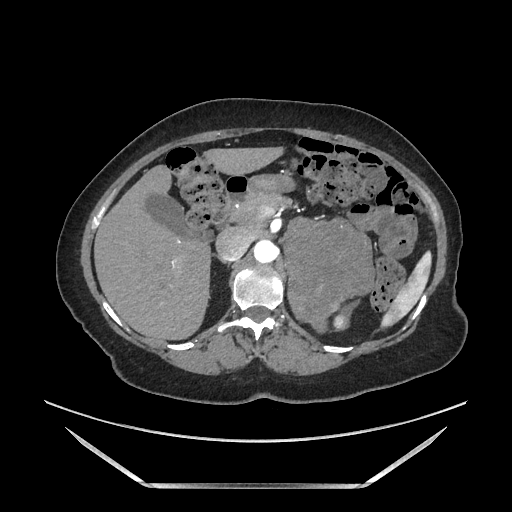
Contrast-enhanced abdominal CT, one axial slice. Position 107 of 205 along the scan axis. Soft-tissue window (W 400 / L 40 HU). 1.25 mm slice thickness. 512 × 512 image matrix, field of view 440 × 440 mm. Female patient. From the clinical record (not read from this slice): diagnosis: adrenocortical carcinoma; tumour side: left adrenal; tumour size at pathology: 12.5 cm; Ki-67 index: 39 %; stage (as recorded): 3.
Annotated regions visible in this slice (semi-automatically segmented with operator editing):
- mass: bounding box [x1, y1, x2, y2] px = [286, 221, 370, 330]